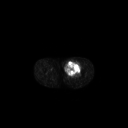
FDG PET of an extremity soft-tissue mass (from a PET/CT study), one axial slice. 128 × 128 image matrix, field of view 700 × 700 mm. Patient: male, 63 years. Case-level facts recorded for this patient, not image findings: histological type: pleiomorphic liposarcoma; grade: high; site of the primary tumour: left thigh.
Outlined on this slice (expert contour drawn on MRI and transferred to this co-registered scan by the dataset authors):
- gross tumour volume including surrounding oedema: bounding box <65,60,82,76> (left, top, right, bottom; pixels)
- gross tumour volume (mass): <65,60,81,76>